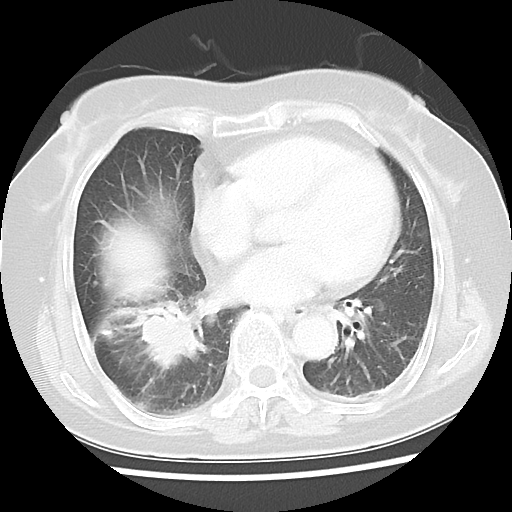
Chest CT, one axial slice. Position 17 of 45 along the scan axis. Reconstruction kernel LUNG. 120 kVp. Lung window (W 1500 / L -600 HU). 512 × 512 image matrix, field of view 312 × 312 mm. Female patient, age 65 years. From the clinical record (not read from this slice): clinical TNM (as recorded): T2 N3 M0.
Annotated regions visible in this slice (bounding box drawn by a radiologist):
- lung tumour (recorded histology: adenocarcinoma): bounding box (x1, y1, x2, y2) in pixels: (136, 300, 207, 384)